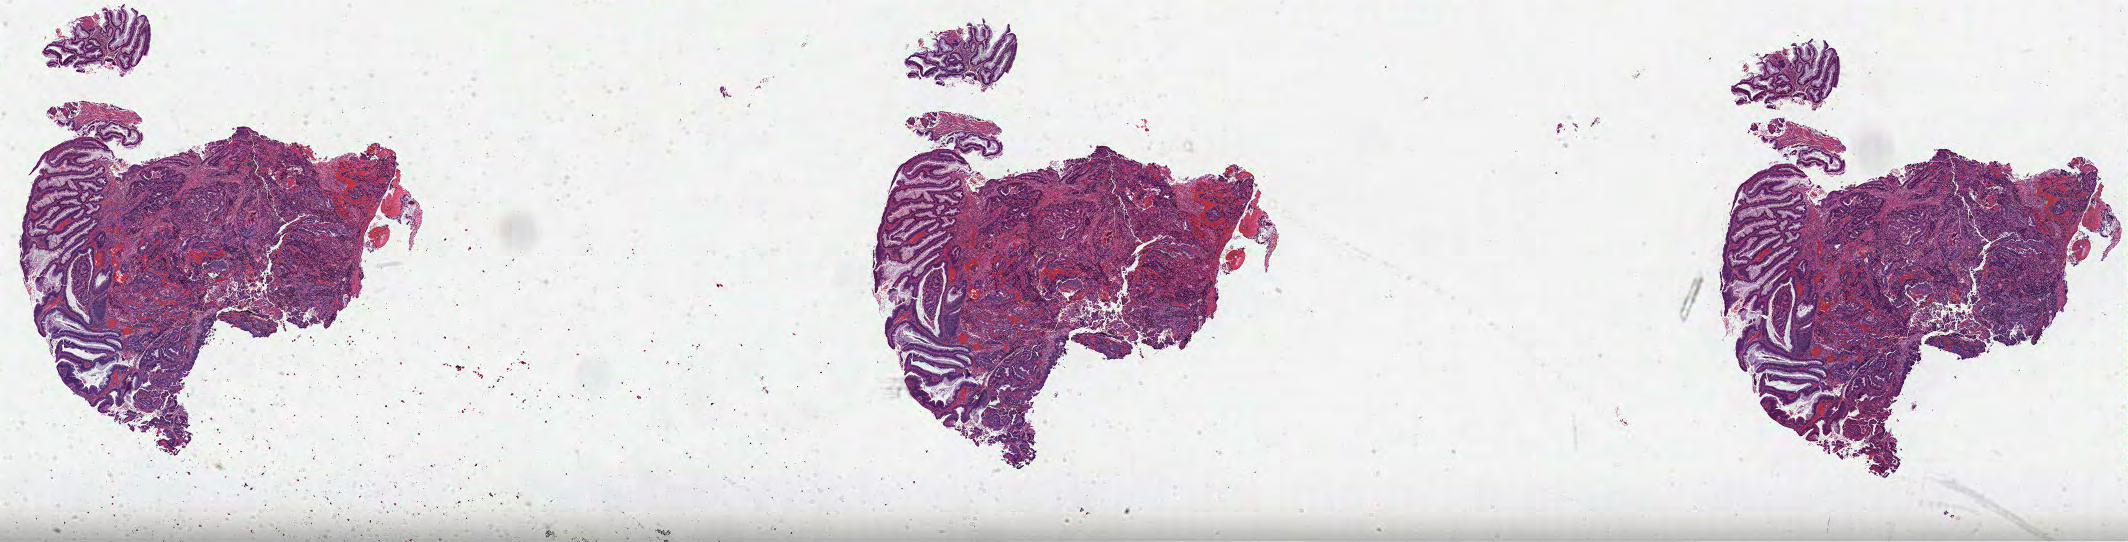
Digitized H&E-stained tissue section (whole slide), low-resolution overview of the scanned area, about 34.3 x 8.7 mm (from a 40x scan); formalin-fixed paraffin-embedded (FFPE) diagnostic section; rectum, primary tumour sample. Female patient; age at initial diagnosis 48 years.
- AJCC pathologic stage: I
- histologic diagnosis: Adenocarcinoma, NOS (rectosigmoid junction)
- lymph nodes positive (case pathology): 0 of 17 examined